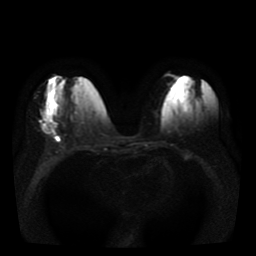
Breast MRI, one axial slice. Diffusion-weighted series; image 2 of 4 stored at this slice position (different b-values; order by instance number). 1.5 T. 5 mm slice thickness. 256 × 256 image matrix, field of view 330 × 330 mm. Female patient.
Structures marked on this image (manually delineated by an expert):
- tumour on diffusion-weighted imaging: bounding box <42,119,58,135> (left, top, right, bottom; pixels)